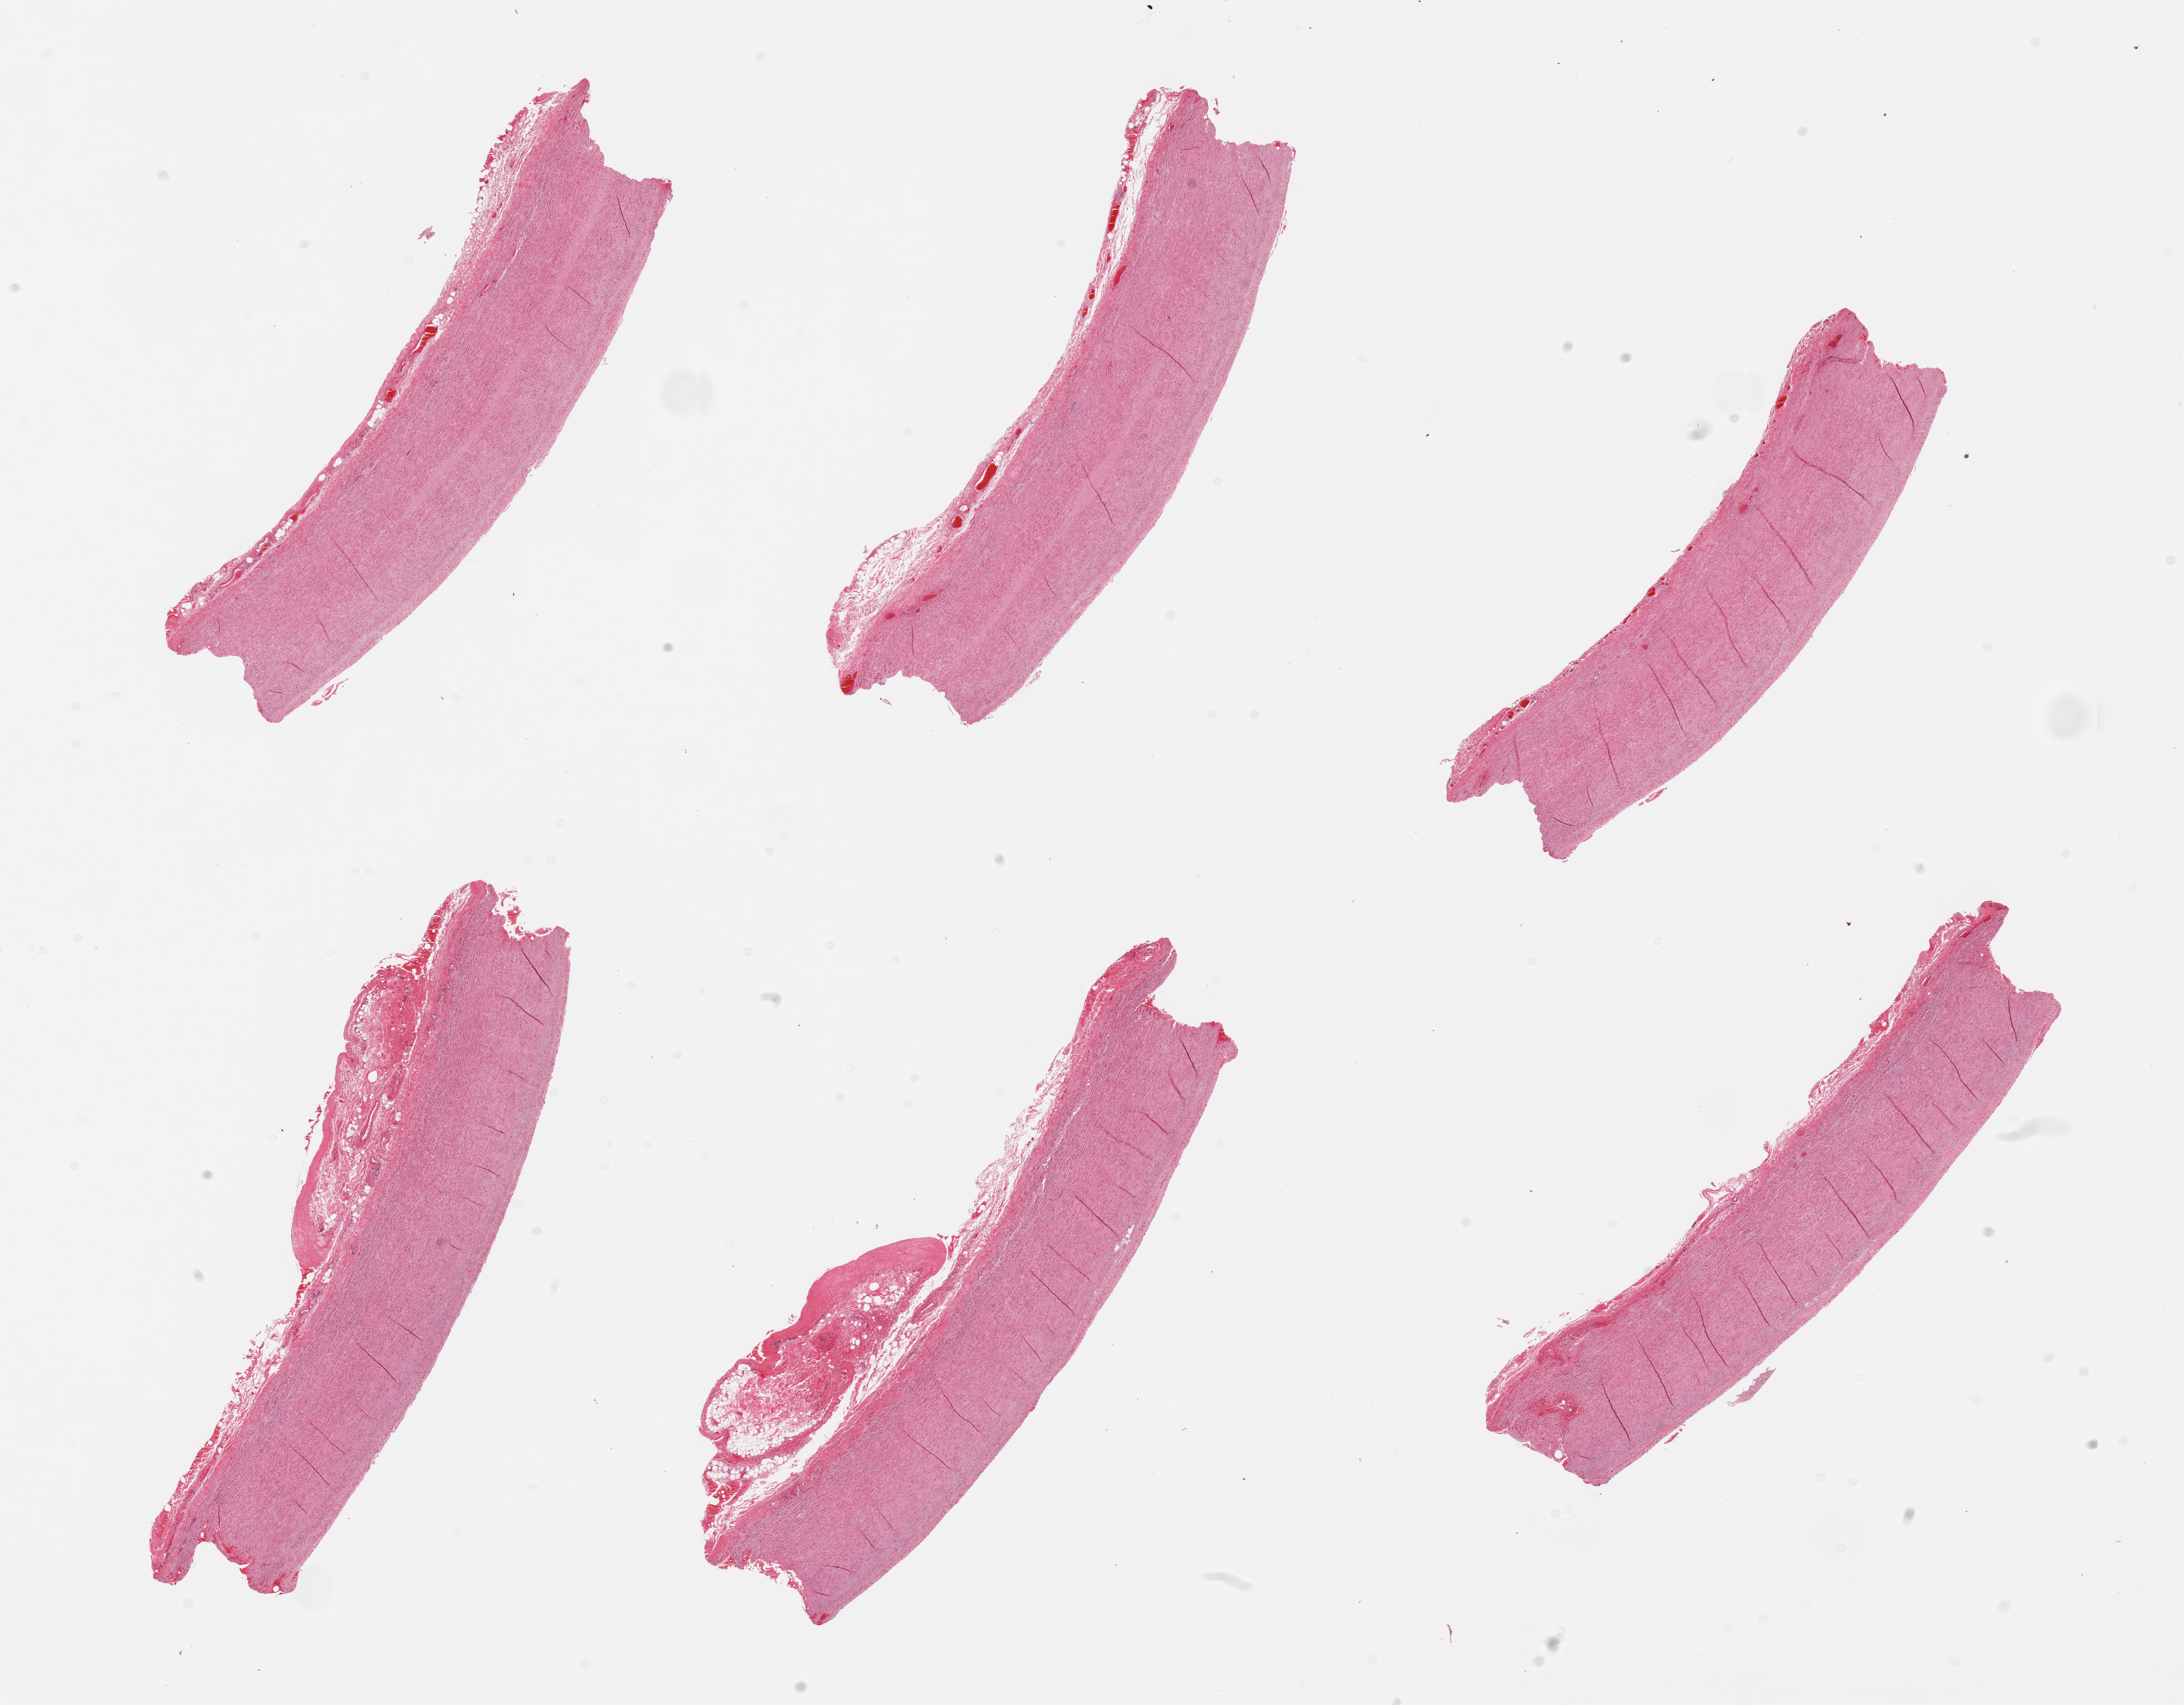
Whole-slide image, haematoxylin and eosin stain, shown as a low-resolution overview of the whole scanned area (about 24.6 x 19.2 mm), PAXgene-fixed, paraffin-embedded tissue, sampled site (target tissue): aorta, donor tissue sample. Donor: male.
Reviewer comment on this tissue sample: 6 pieces; no plaques; periaortic fibrofatty tissue in 2.